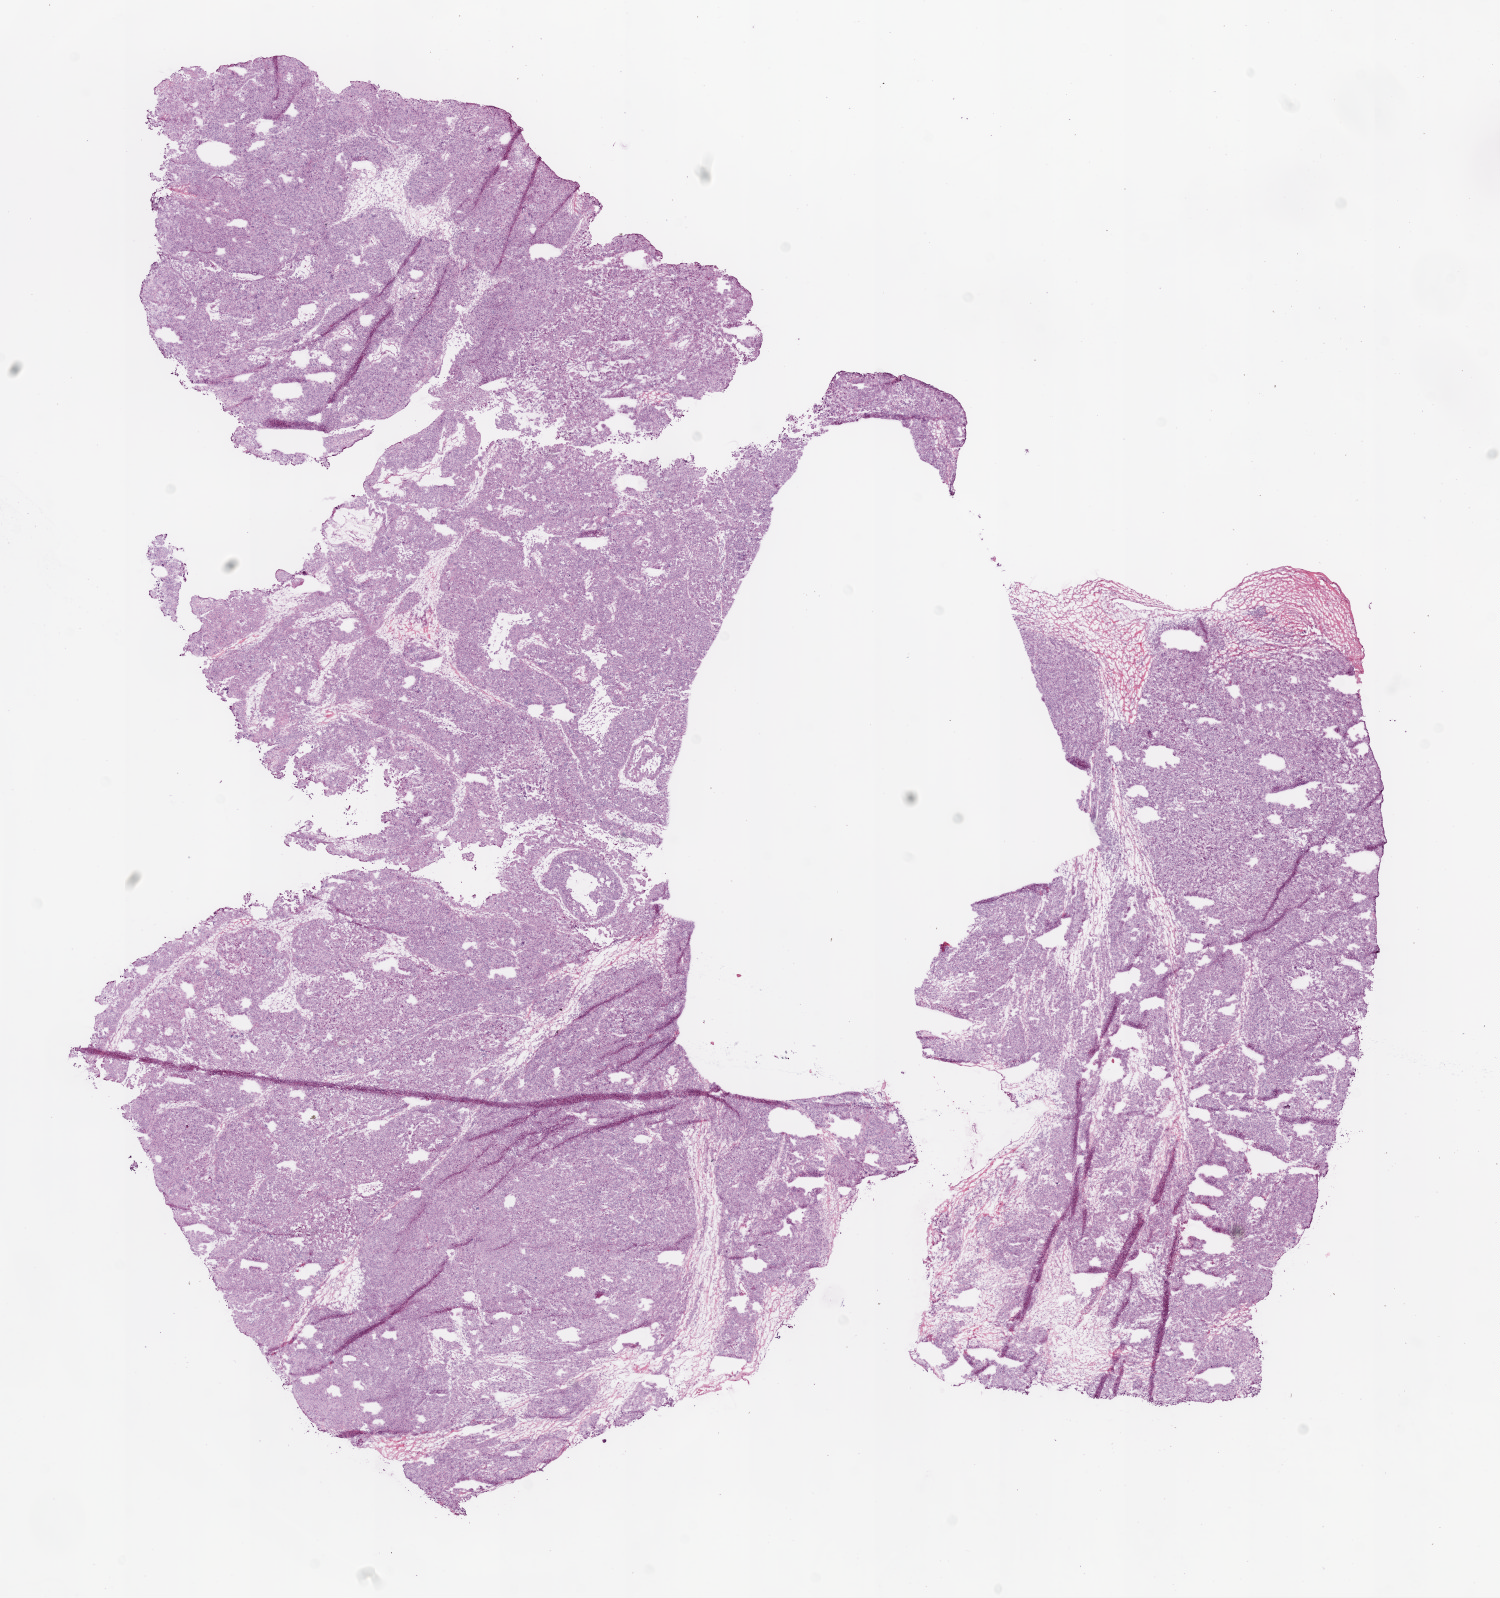
Whole-slide histology image, H&E, shown as a low-resolution overview of the whole scanned area (about 12.0 x 12.8 mm, acquisition: 20x scan). Frozen section from the bottom of the tissue portion. Ovary, primary tumour sample. Female, age 55 years at initial diagnosis. Histologic grade: G3 (poorly differentiated). Pathologist review of this section (percent, as recorded): tumour cells 95%, tumour nuclei 80%, normal cells 0%, stromal cells 5%, necrosis 0%. Inflammatory infiltration, as recorded: lymphocyte infiltration 15%.
FIGO stage: IIIC. Pathologic diagnosis: Serous cystadenocarcinoma, NOS. Laterality: right.